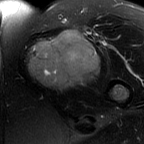
MRI of an extremity soft-tissue mass, one axial slice; position 45 of 60 along the scan axis; T2-weighted fat-saturated; MR volume resampled by the dataset authors to the PET/CT grid (not the native acquisition matrix); 3.27 mm slice thickness; 144 × 144 image matrix, field of view 141 × 141 mm. Female patient. From the clinical record (not read from this slice): histological type: pleiomorphic leiomyosarcoma; grade: intermediate; site of the primary tumour: left thigh.
Annotated regions visible in this slice (expert contour drawn on MRI and transferred to this co-registered scan by the dataset authors):
- gross tumour volume including surrounding oedema: bounding box [x1, y1, x2, y2] px = [27, 29, 99, 89]
- gross tumour volume (mass): [27, 29, 99, 89]